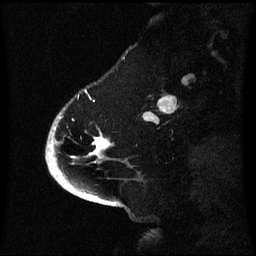
Breast MRI (dynamic contrast-enhanced), one sagittal slice. Slice 16 of 60 in the series (ordered by position). Dynamic contrast-enhanced series, image 2 of 3 at this slice position (ordered by acquisition). 1.5 T. TE 4.2 ms, TR 8.4 ms. 2.1 mm slice thickness. 256 × 256 image matrix, field of view 220 × 220 mm. Female patient, age 53 years. Case-level facts recorded for this patient, not image findings: setting: breast cancer imaged before/during neoadjuvant chemotherapy; receptor status: HR-positive, HER2-negative.
Outlined on this slice (semi-automatically segmented with operator editing):
- analysis volume of interest (the breast-tissue region the enhancement analysis was run in; not a lesion): box from (x=52, y=108) to (x=114, y=171) px
- tumour enhancement mask (voxels above the 70 % enhancement threshold inside the analysis volume of interest): (x=52, y=138)–(x=112, y=167)